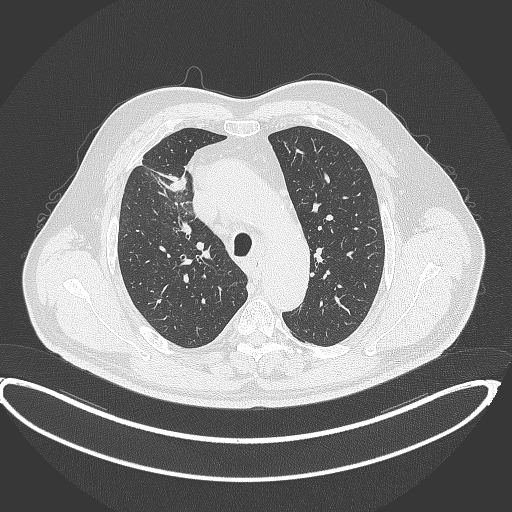
Chest CT, one axial slice. Position 303 of 390 along the scan axis. Reconstruction kernel B70f. 120 kVp. Lung window (W 1500 / L -600 HU). 1 mm slice thickness. 512 × 512 image matrix. Male patient, age 62 years. Case-level facts recorded for this patient, not image findings: clinical TNM (as recorded): T1c N3 M1c.
Outlined on this slice (rectangle marked by the reading radiologist):
- lung tumour (recorded histology: adenocarcinoma): bounding box [x1, y1, x2, y2] px = [166, 174, 191, 192]